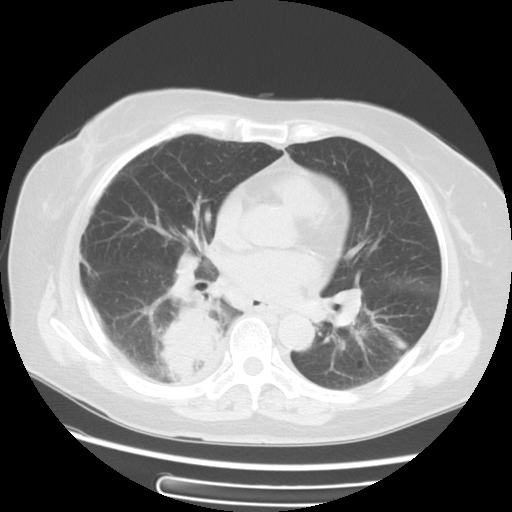
Chest CT, one axial slice; slice 30 of 57 in the series (ordered by position); reconstruction kernel STANDARD; 120 kVp; lung window (W 1500 / L -600 HU); 5 mm slice thickness; 512 × 512 image matrix, field of view 350 × 350 mm. Female patient, age 69 years. Case-level facts recorded for this patient, not image findings: clinical TNM (as recorded): T2 N1 M1a.
Annotated regions visible in this slice (bounding box drawn by a radiologist):
- lung tumour (recorded histology: adenocarcinoma): box from (x=154, y=304) to (x=228, y=393) px